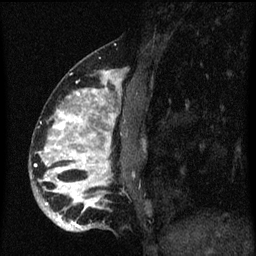
Breast MRI (dynamic contrast-enhanced), one sagittal slice; slice 21 of 60 in the series (ordered by position); dynamic contrast-enhanced series, image 2 of 3 at this slice position (ordered by acquisition); 1.5 T; TE 4.2 ms, TR 8.4 ms; 2 mm slice thickness; 256 × 256 image matrix. Patient: female, 34 years. From the clinical record (not read from this slice): setting: breast cancer imaged before/during neoadjuvant chemotherapy; receptor status: HR-positive, HER2-negative.
Annotated regions visible in this slice (semi-automatic segmentation, software-assisted and operator-edited):
- analysis volume of interest (the breast-tissue region the enhancement analysis was run in; not a lesion): bounding box (x1, y1, x2, y2) in pixels: (30, 58, 131, 233)
- tumour enhancement mask (voxels above the 70 % enhancement threshold inside the analysis volume of interest): (40, 72, 117, 229)